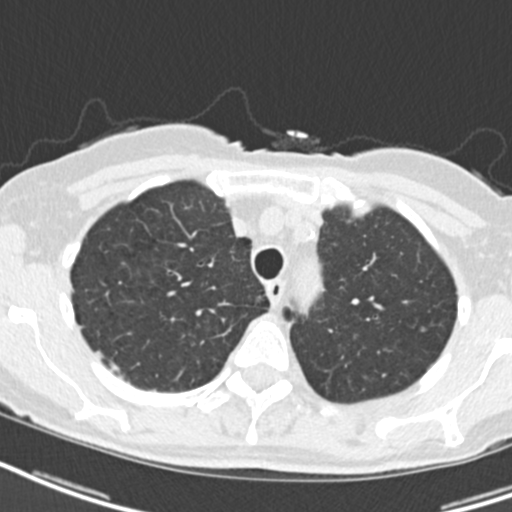
Axial slice from a low-dose chest CT screening exam. Baseline annual screen. Lung window (W 1500 / L -600 HU). 2 mm slice thickness. Standard (soft-tissue) reconstruction kernel (B30f). 512 × 512 image matrix. Female, age 68 years at enrolment. Current smoker at enrolment.
- Lesion marked by an expert reader, bounding box <248,285,275,312> (left, top, right, bottom; pixels).
- No non-calcified nodule or mass ≥4 mm was recorded by the screening reader at this exam.
- Lung cancer was diagnosed 807 days after this screen: squamous cell carcinoma, NOS, right upper lobe, mediastinum, poorly differentiated (G3), stage IIIB (AJCC 6th edition), 43 mm at pathology.